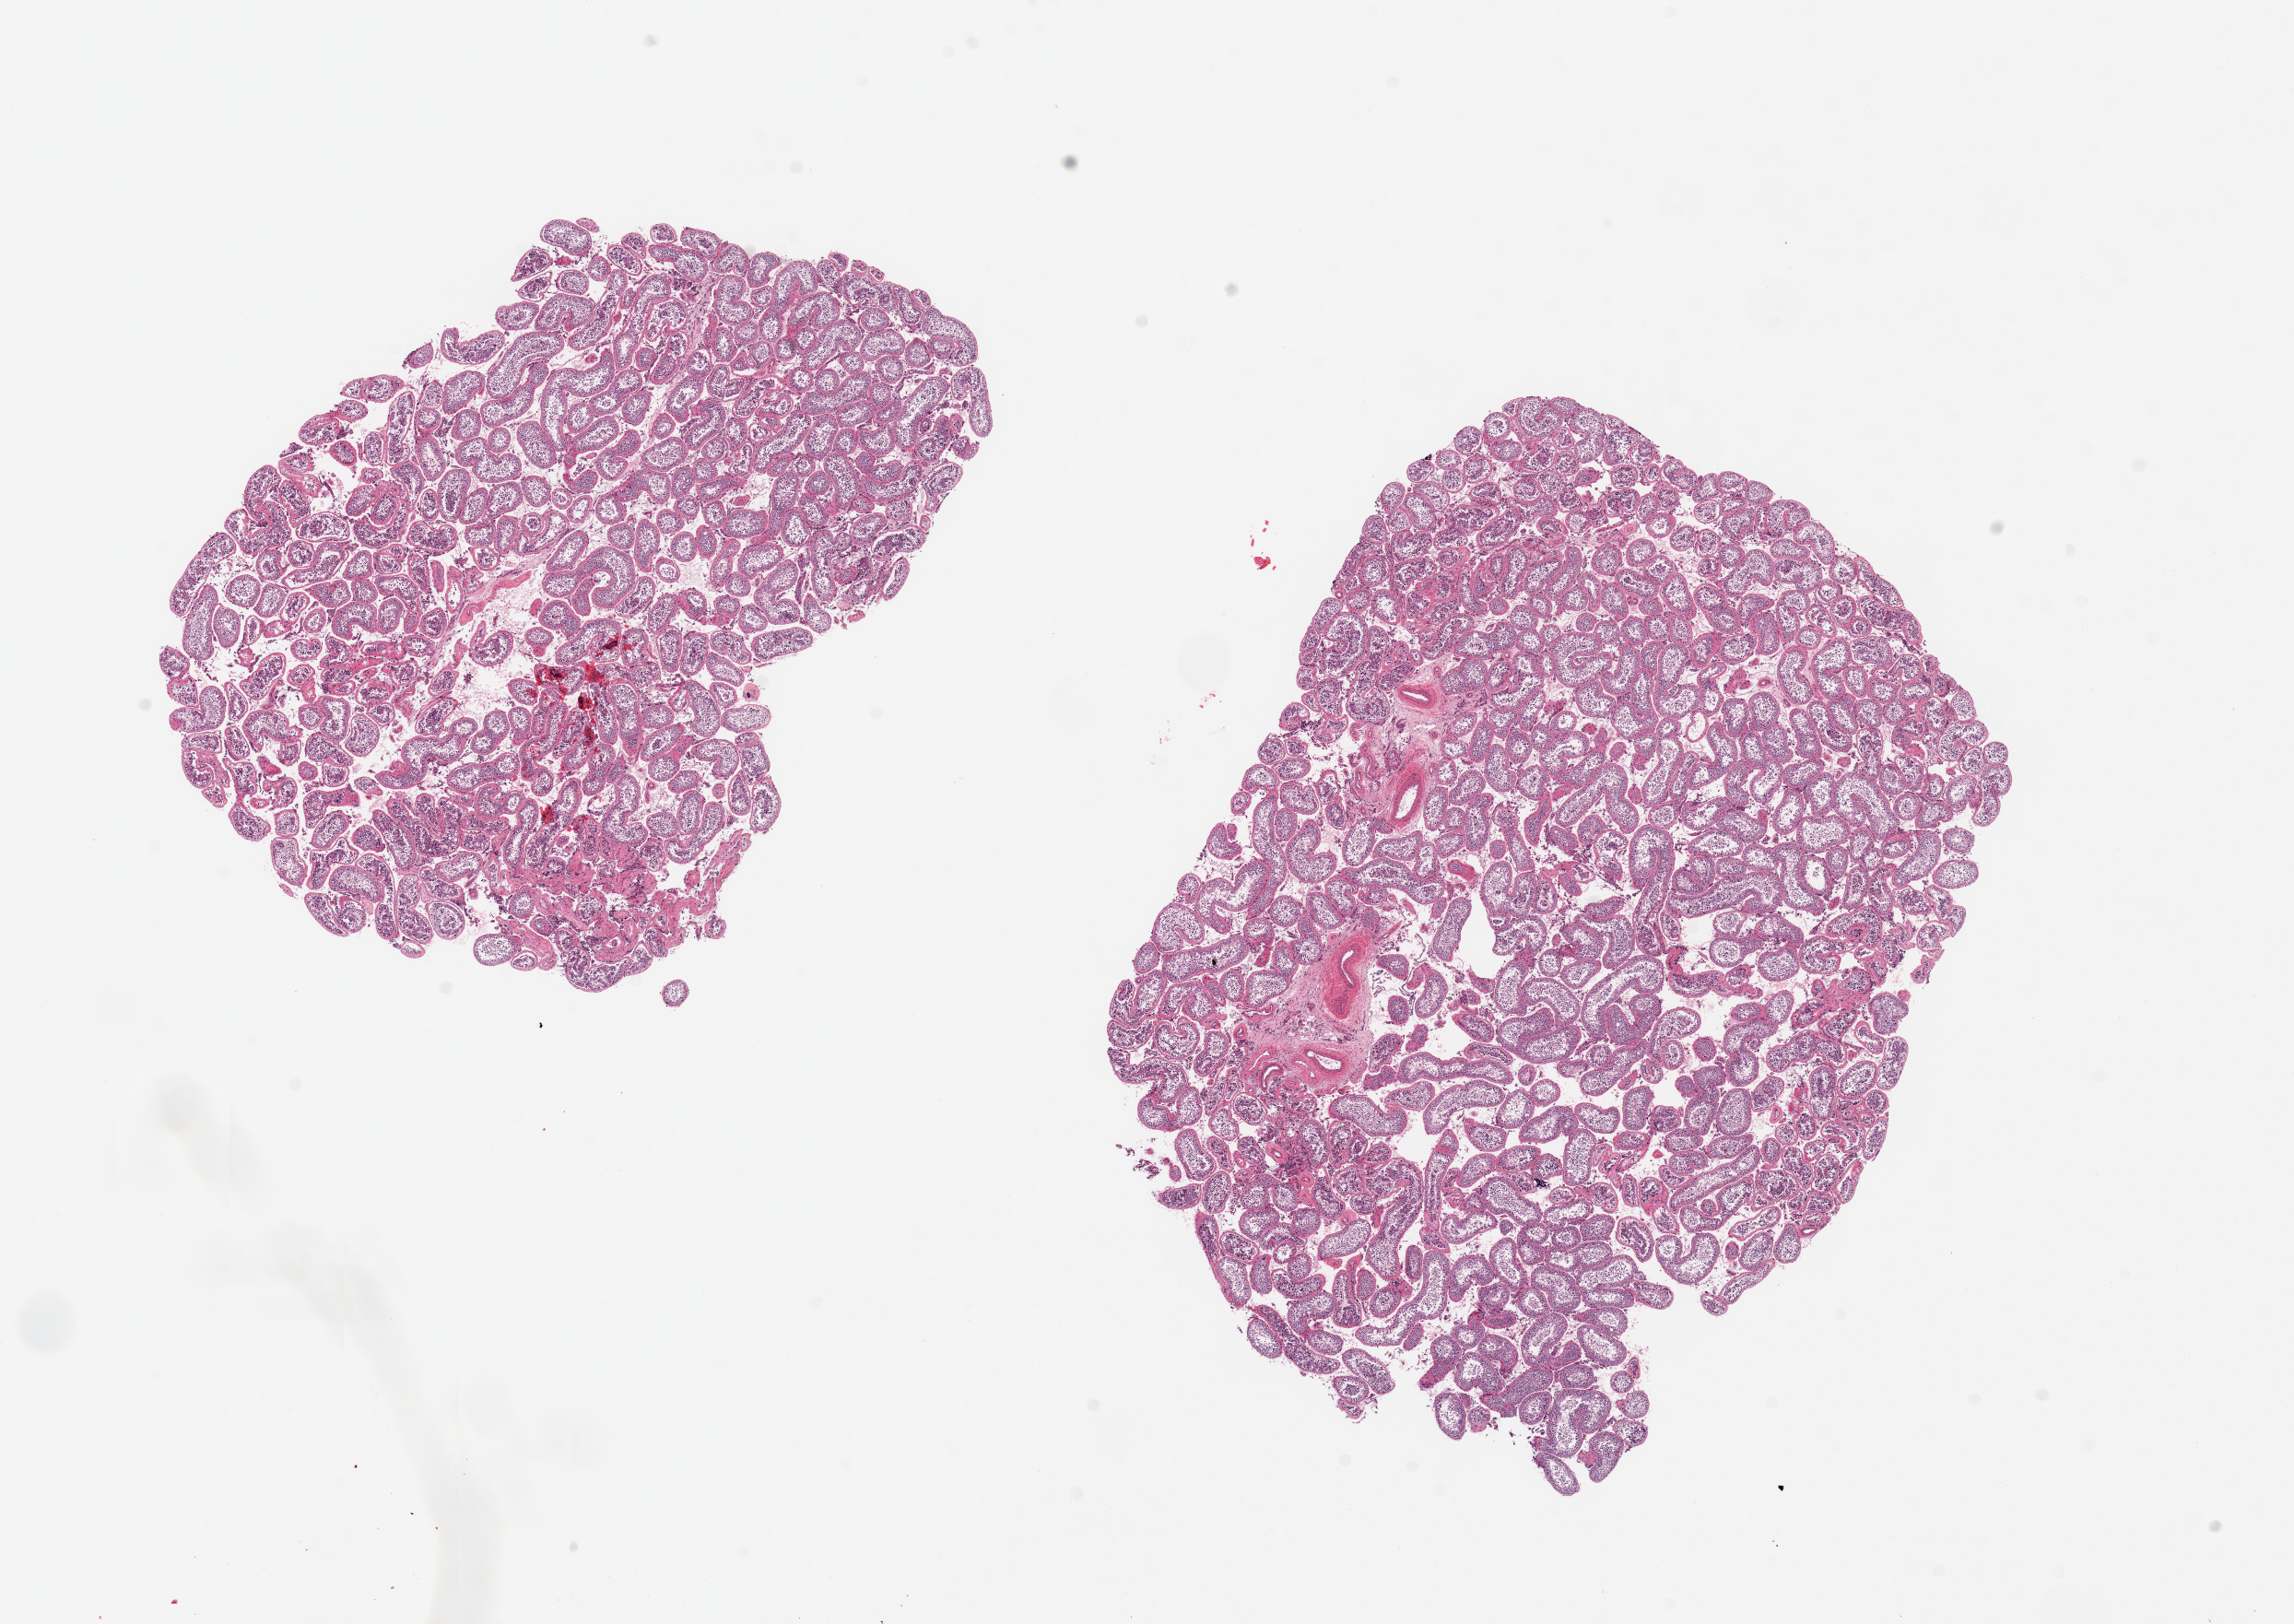
Whole-slide image, haematoxylin and eosin stain, brightfield — whole scanned area (about 19.7 x 13.9 mm) shown as a low-resolution overview; PAXgene-fixed, paraffin-embedded tissue; target tissue: testis; donor tissue sample. Donor sex: male.
Reviewer comment on this tissue sample: 2 pieces, 7x5.5 & 9x7mm.